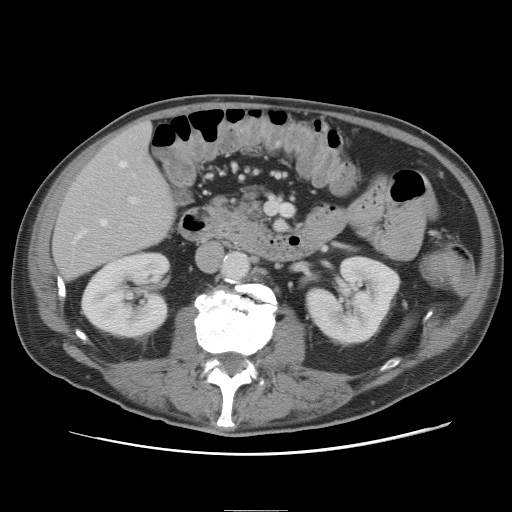
Contrast-enhanced abdominal CT, one axial slice; intravenous contrast given; soft-tissue window (W 400 / L 40 HU); 5 mm slice thickness; 512 × 512 image matrix, field of view 375 × 375 mm. Male patient, age 69 years. Case-level facts recorded for this patient, not image findings: diagnosis: colorectal cancer liver metastases, imaged before liver resection; multiple liver metastases: no; largest metastasis: 8.5 cm.
Outlined on this slice (manually delineated by an expert):
- hepatic veins: bounding box <78,161,127,238> (left, top, right, bottom; pixels)
- liver: <52,122,174,278>
- planned liver remnant (the part of the liver to remain after resection): <54,122,174,278>
- portal vein (with intrahepatic branches): <130,197,138,204>